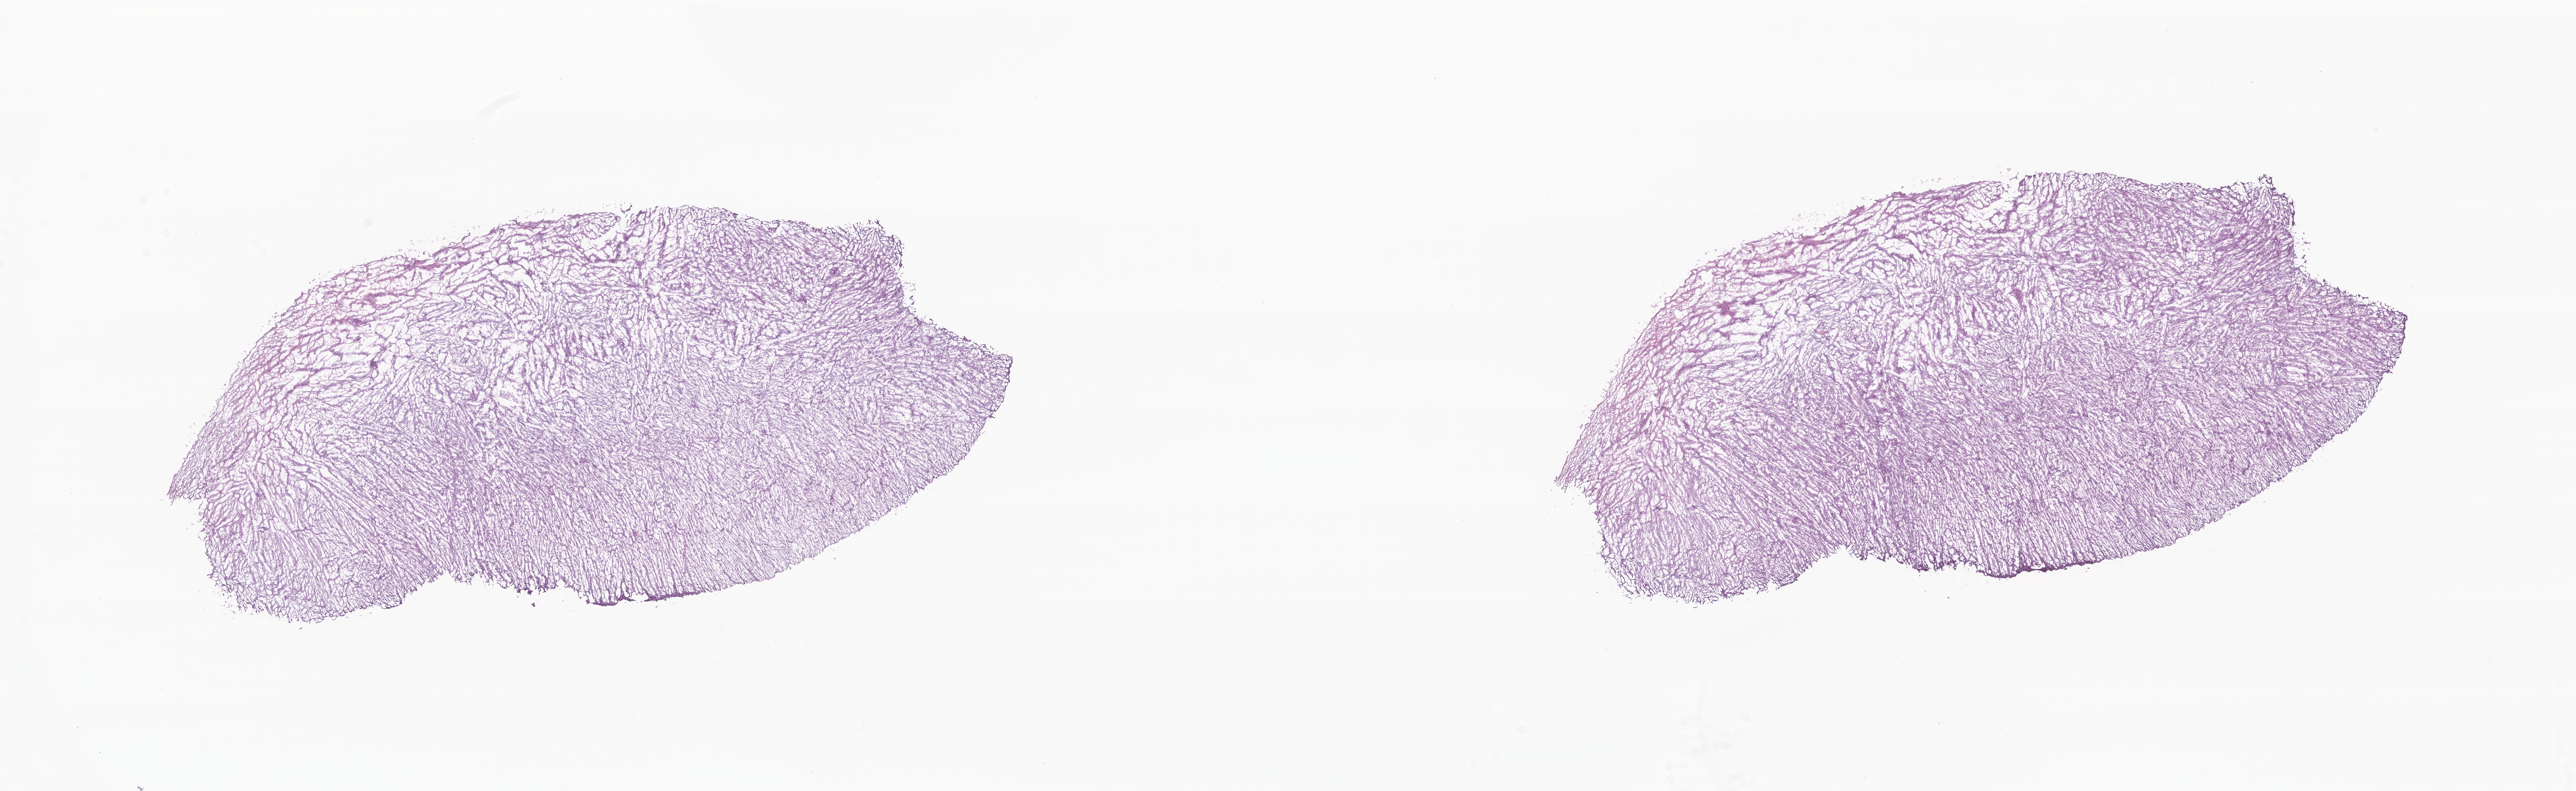
Whole-slide image, H&E stain of tumor tissue from the brain — a low-resolution overview of the entire scanned area, about 28.2 x 8.7 mm, cryosection (OCT / tissue freezing medium). Patient female; age 295 days.
- recorded diagnosis: Glioma, malignant